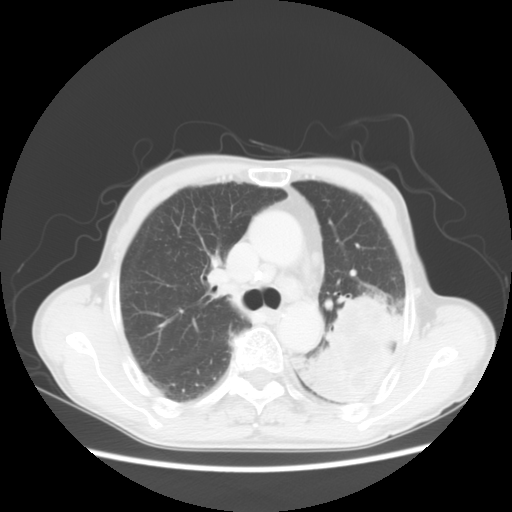
Chest CT, one axial slice; position 35 of 51 along the scan axis; lung window (W 1500 / L -600 HU); 5 mm slice thickness; 512 × 512 image matrix, field of view 360 × 360 mm. Male patient, age 64 years. Case-level facts recorded for this patient, not image findings: clinical TNM (as recorded): T4 N0 M0.
Structures marked on this image (rectangle marked by the reading radiologist):
- lung tumour (recorded histology: squamous cell carcinoma): bounding box (x1, y1, x2, y2) in pixels: (299, 283, 414, 429)